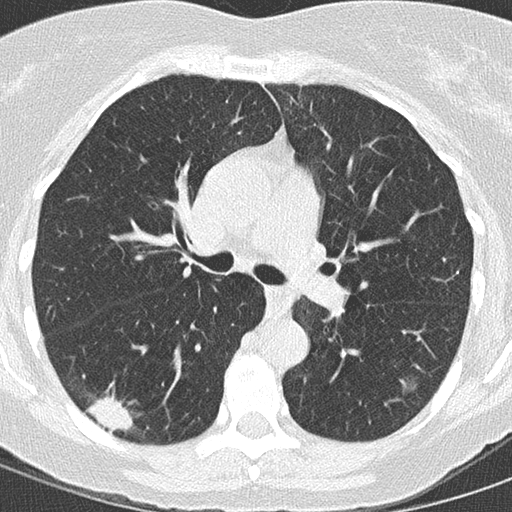
Axial slice from a low-dose chest CT screening exam. Baseline annual screen. Lung window (W 1500 / L -600 HU). 512 × 512 image matrix. Female participant, aged 59 years at enrolment.
Expert-annotated lung lesion, box from (x=70, y=386) to (x=146, y=444) px. The exam's reader record, not a measurement of the box and not confirmed to be the same lesion: non-calcified nodule or mass ≥4 mm, right lower lobe, 24 × 15 mm, spiculated (stellate) margins, soft tissue attenuation. Official screen result: positive, change unspecified: nodule(s) >= 4 mm or enlarging nodule(s), mass(es), or other non-specific abnormalities suspicious for lung cancer. Participant outcome: lung cancer diagnosed 12 days after this screen — adenocarcinoma, NOS, right lower lobe, moderately differentiated (G2), stage IIB (AJCC 6th edition), 22 mm at pathology.